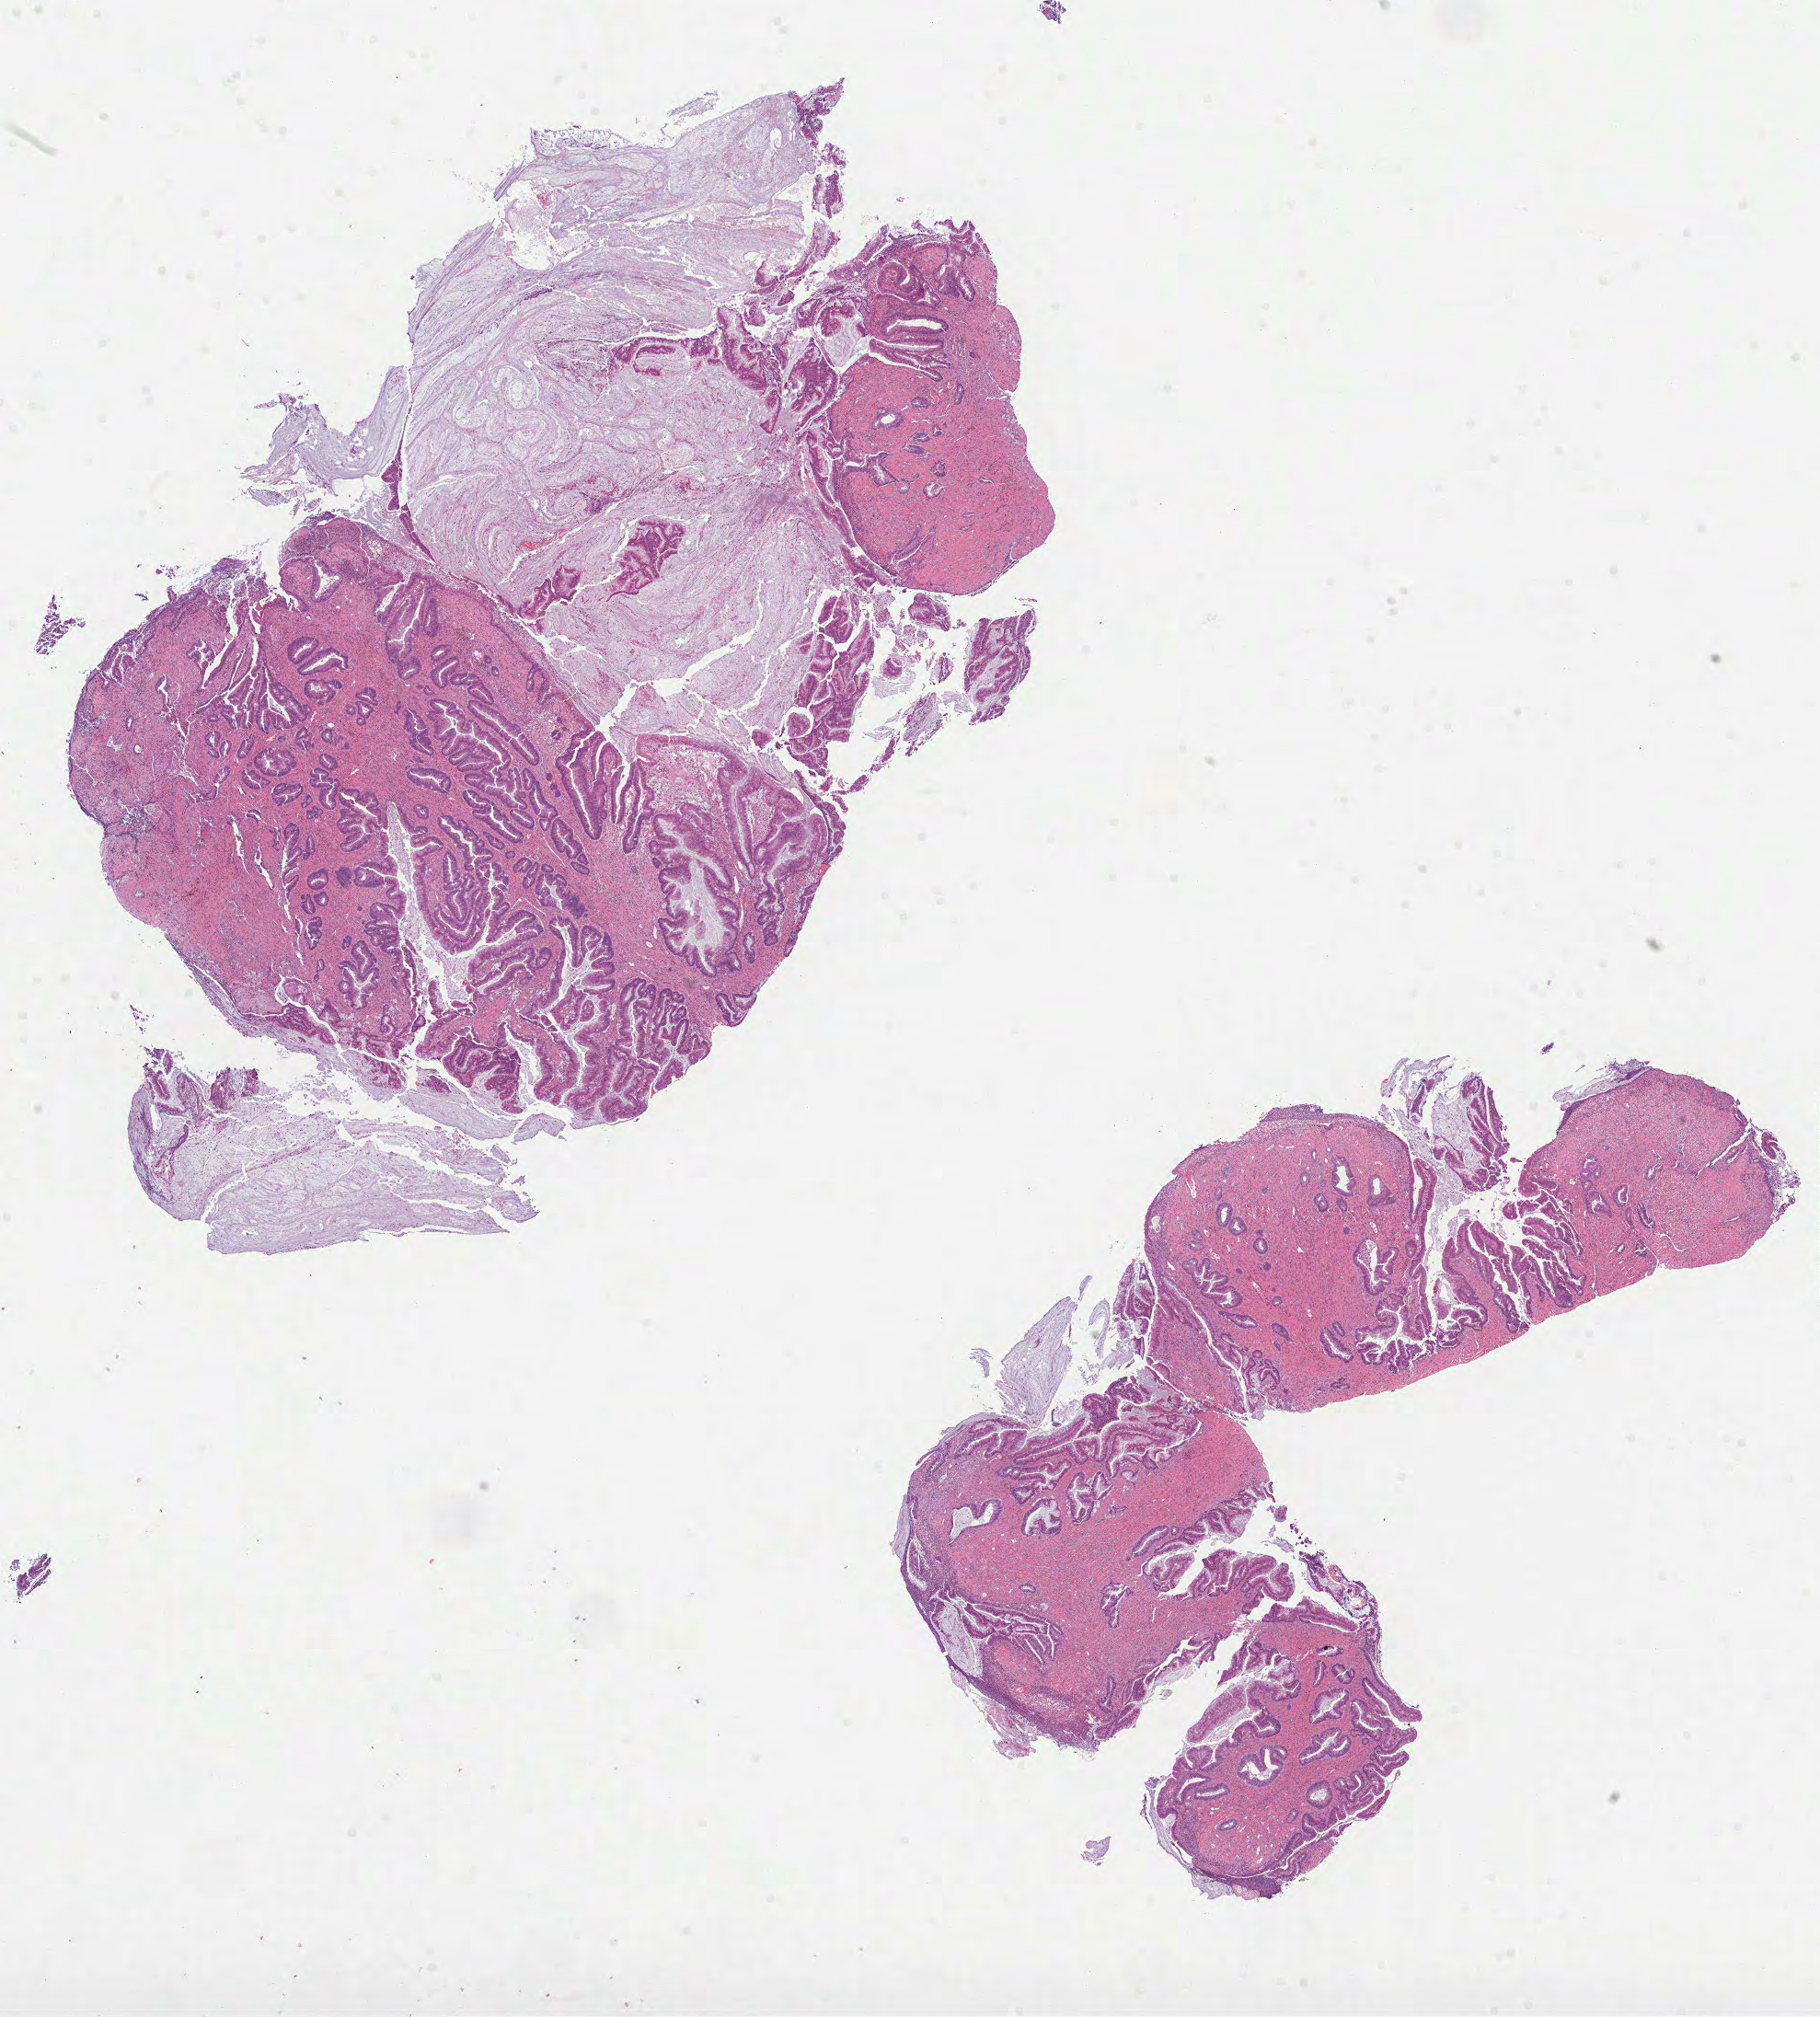
Digitized H&E-stained tissue section (whole slide) — a low-resolution overview of the entire scanned area, about 16.0 x 17.7 mm (slide scanned at 40x). Formalin-fixed paraffin-embedded (FFPE) diagnostic section. Pancreas, primary tumour sample. Male patient; age at initial diagnosis 77 years. Histologic grade: G1 (well differentiated).
Histologic diagnosis: Adenocarcinoma, NOS (head of pancreas). Lymph nodes positive (case pathology): 1 of 9 examined. TNM: T3 N1 MX. AJCC pathologic stage: IIB.